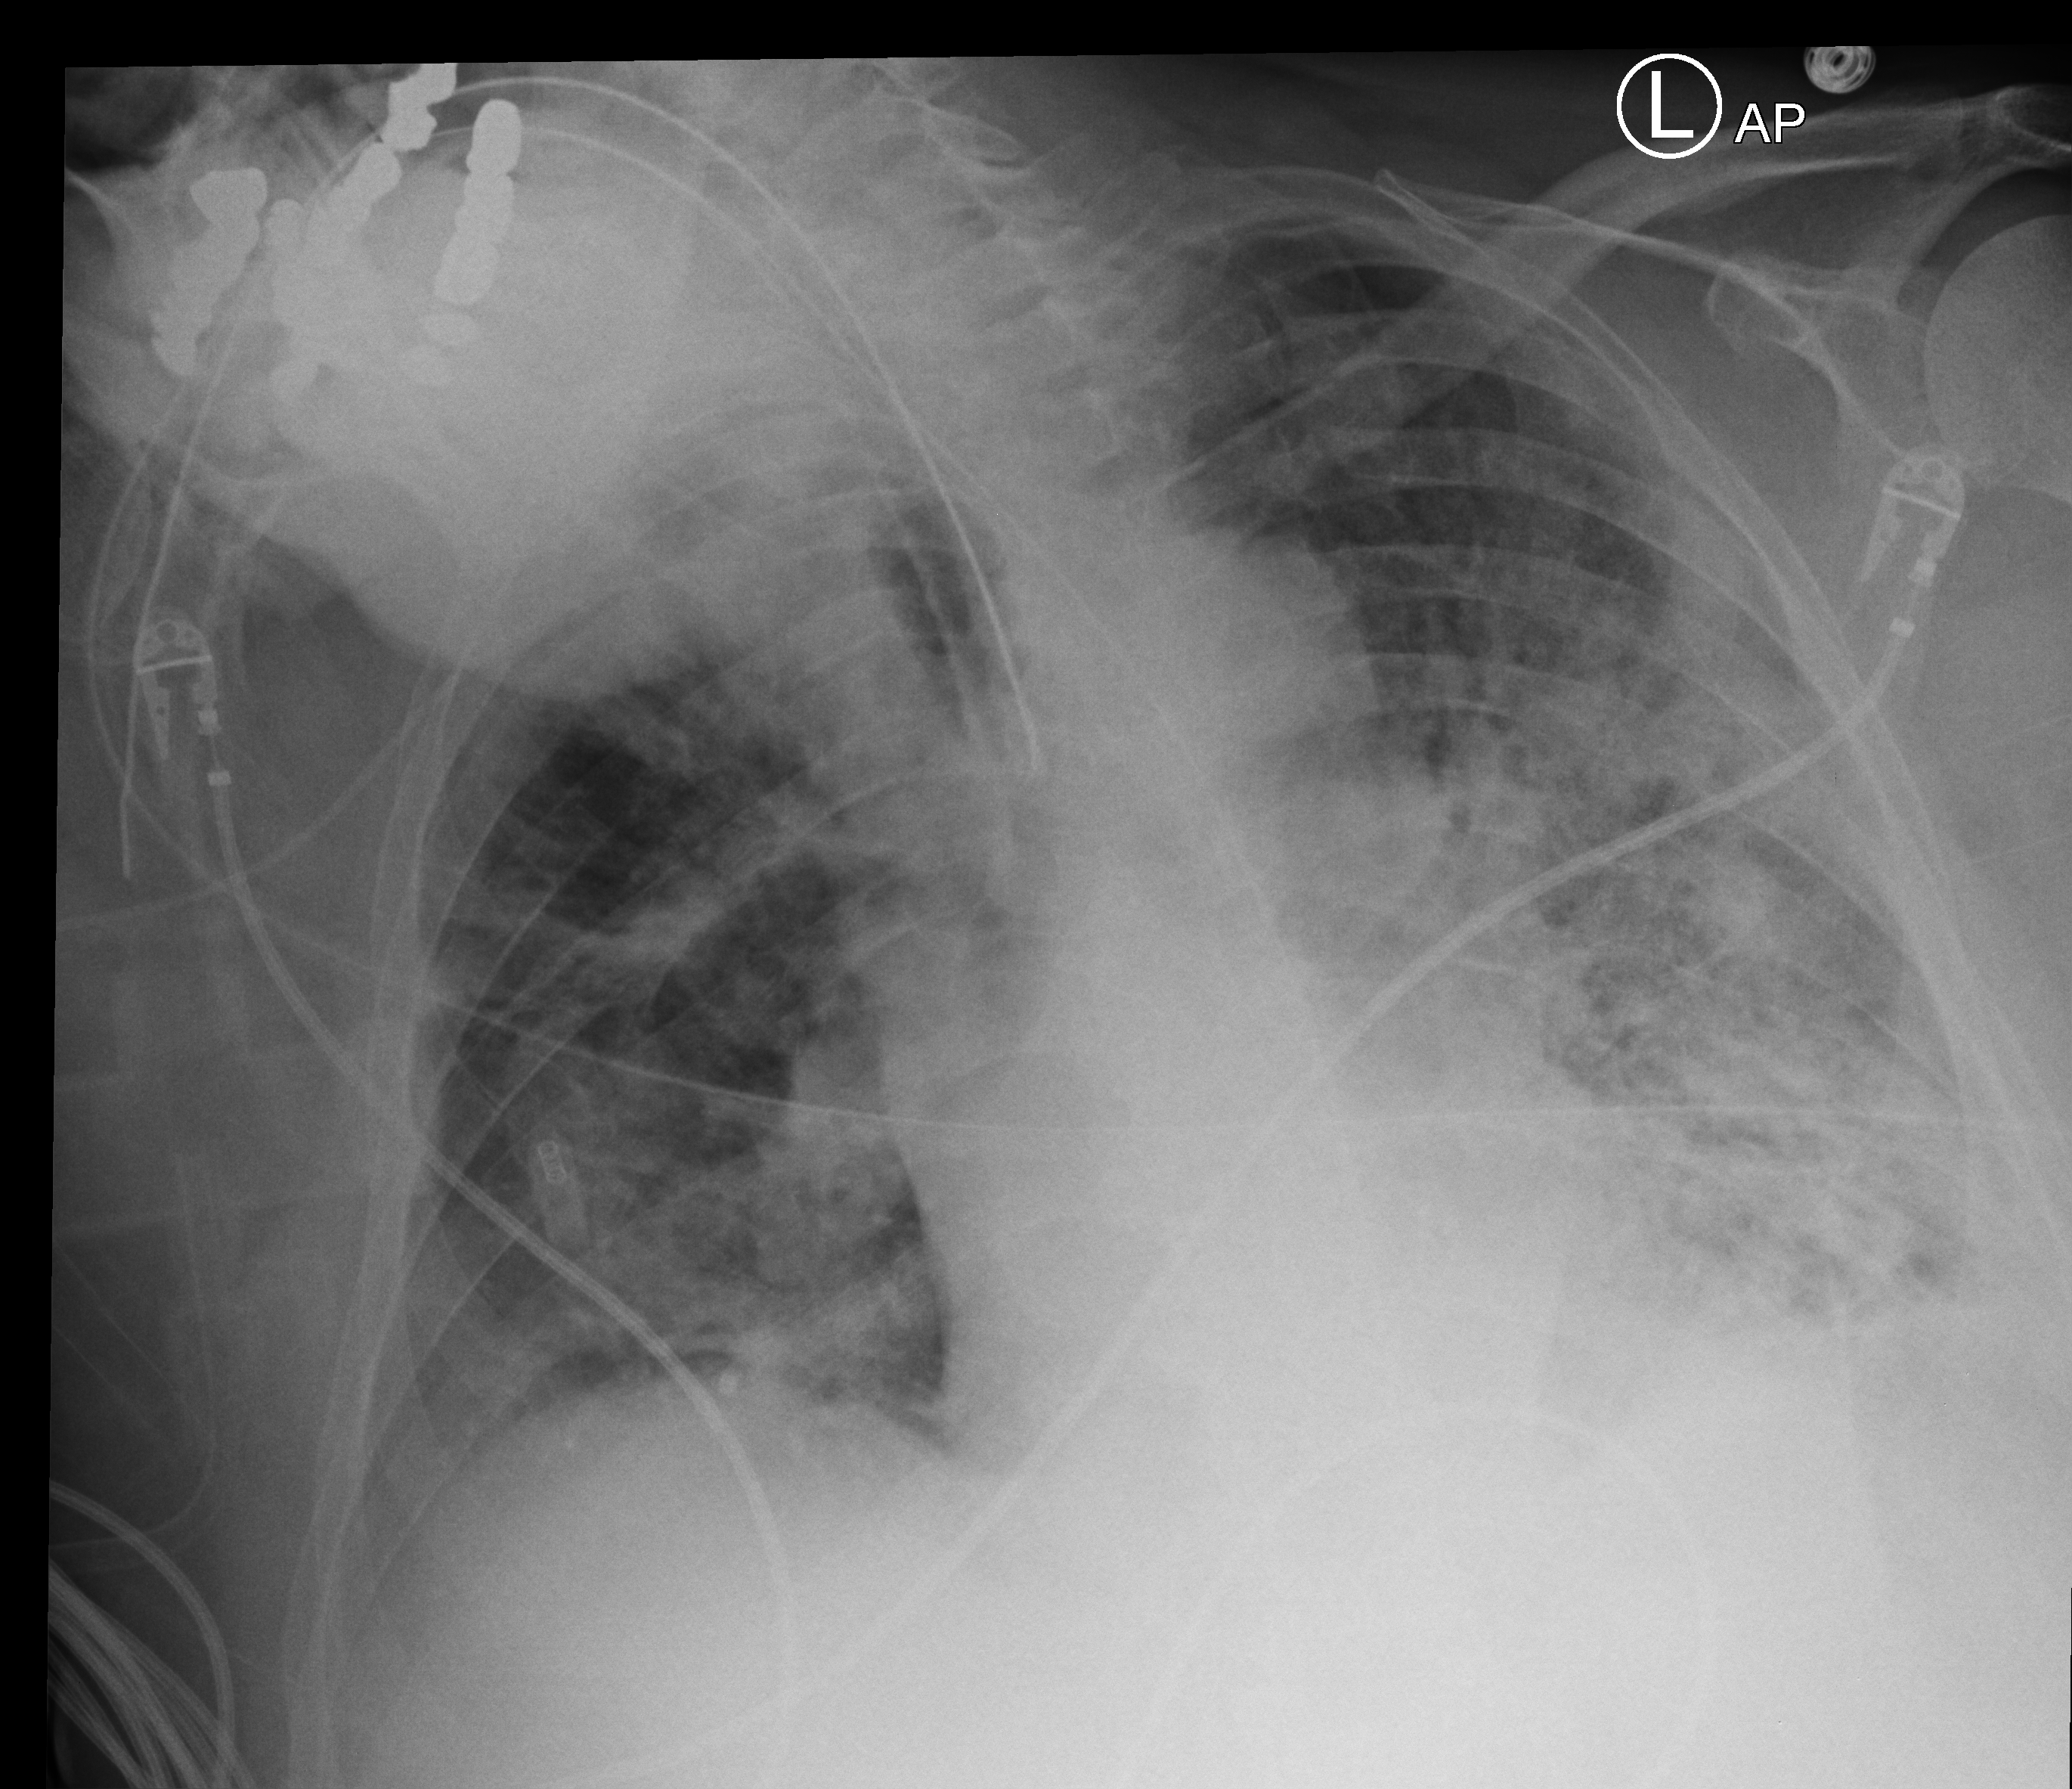
Chest X-ray (portable); anteroposterior (AP) projection. Male patient hospitalised with COVID-19, age 60–74 years.
Hospital-stay facts (about this admission, not read from this image; timing relative to this image not recorded):
- length of hospital stay: 24 days